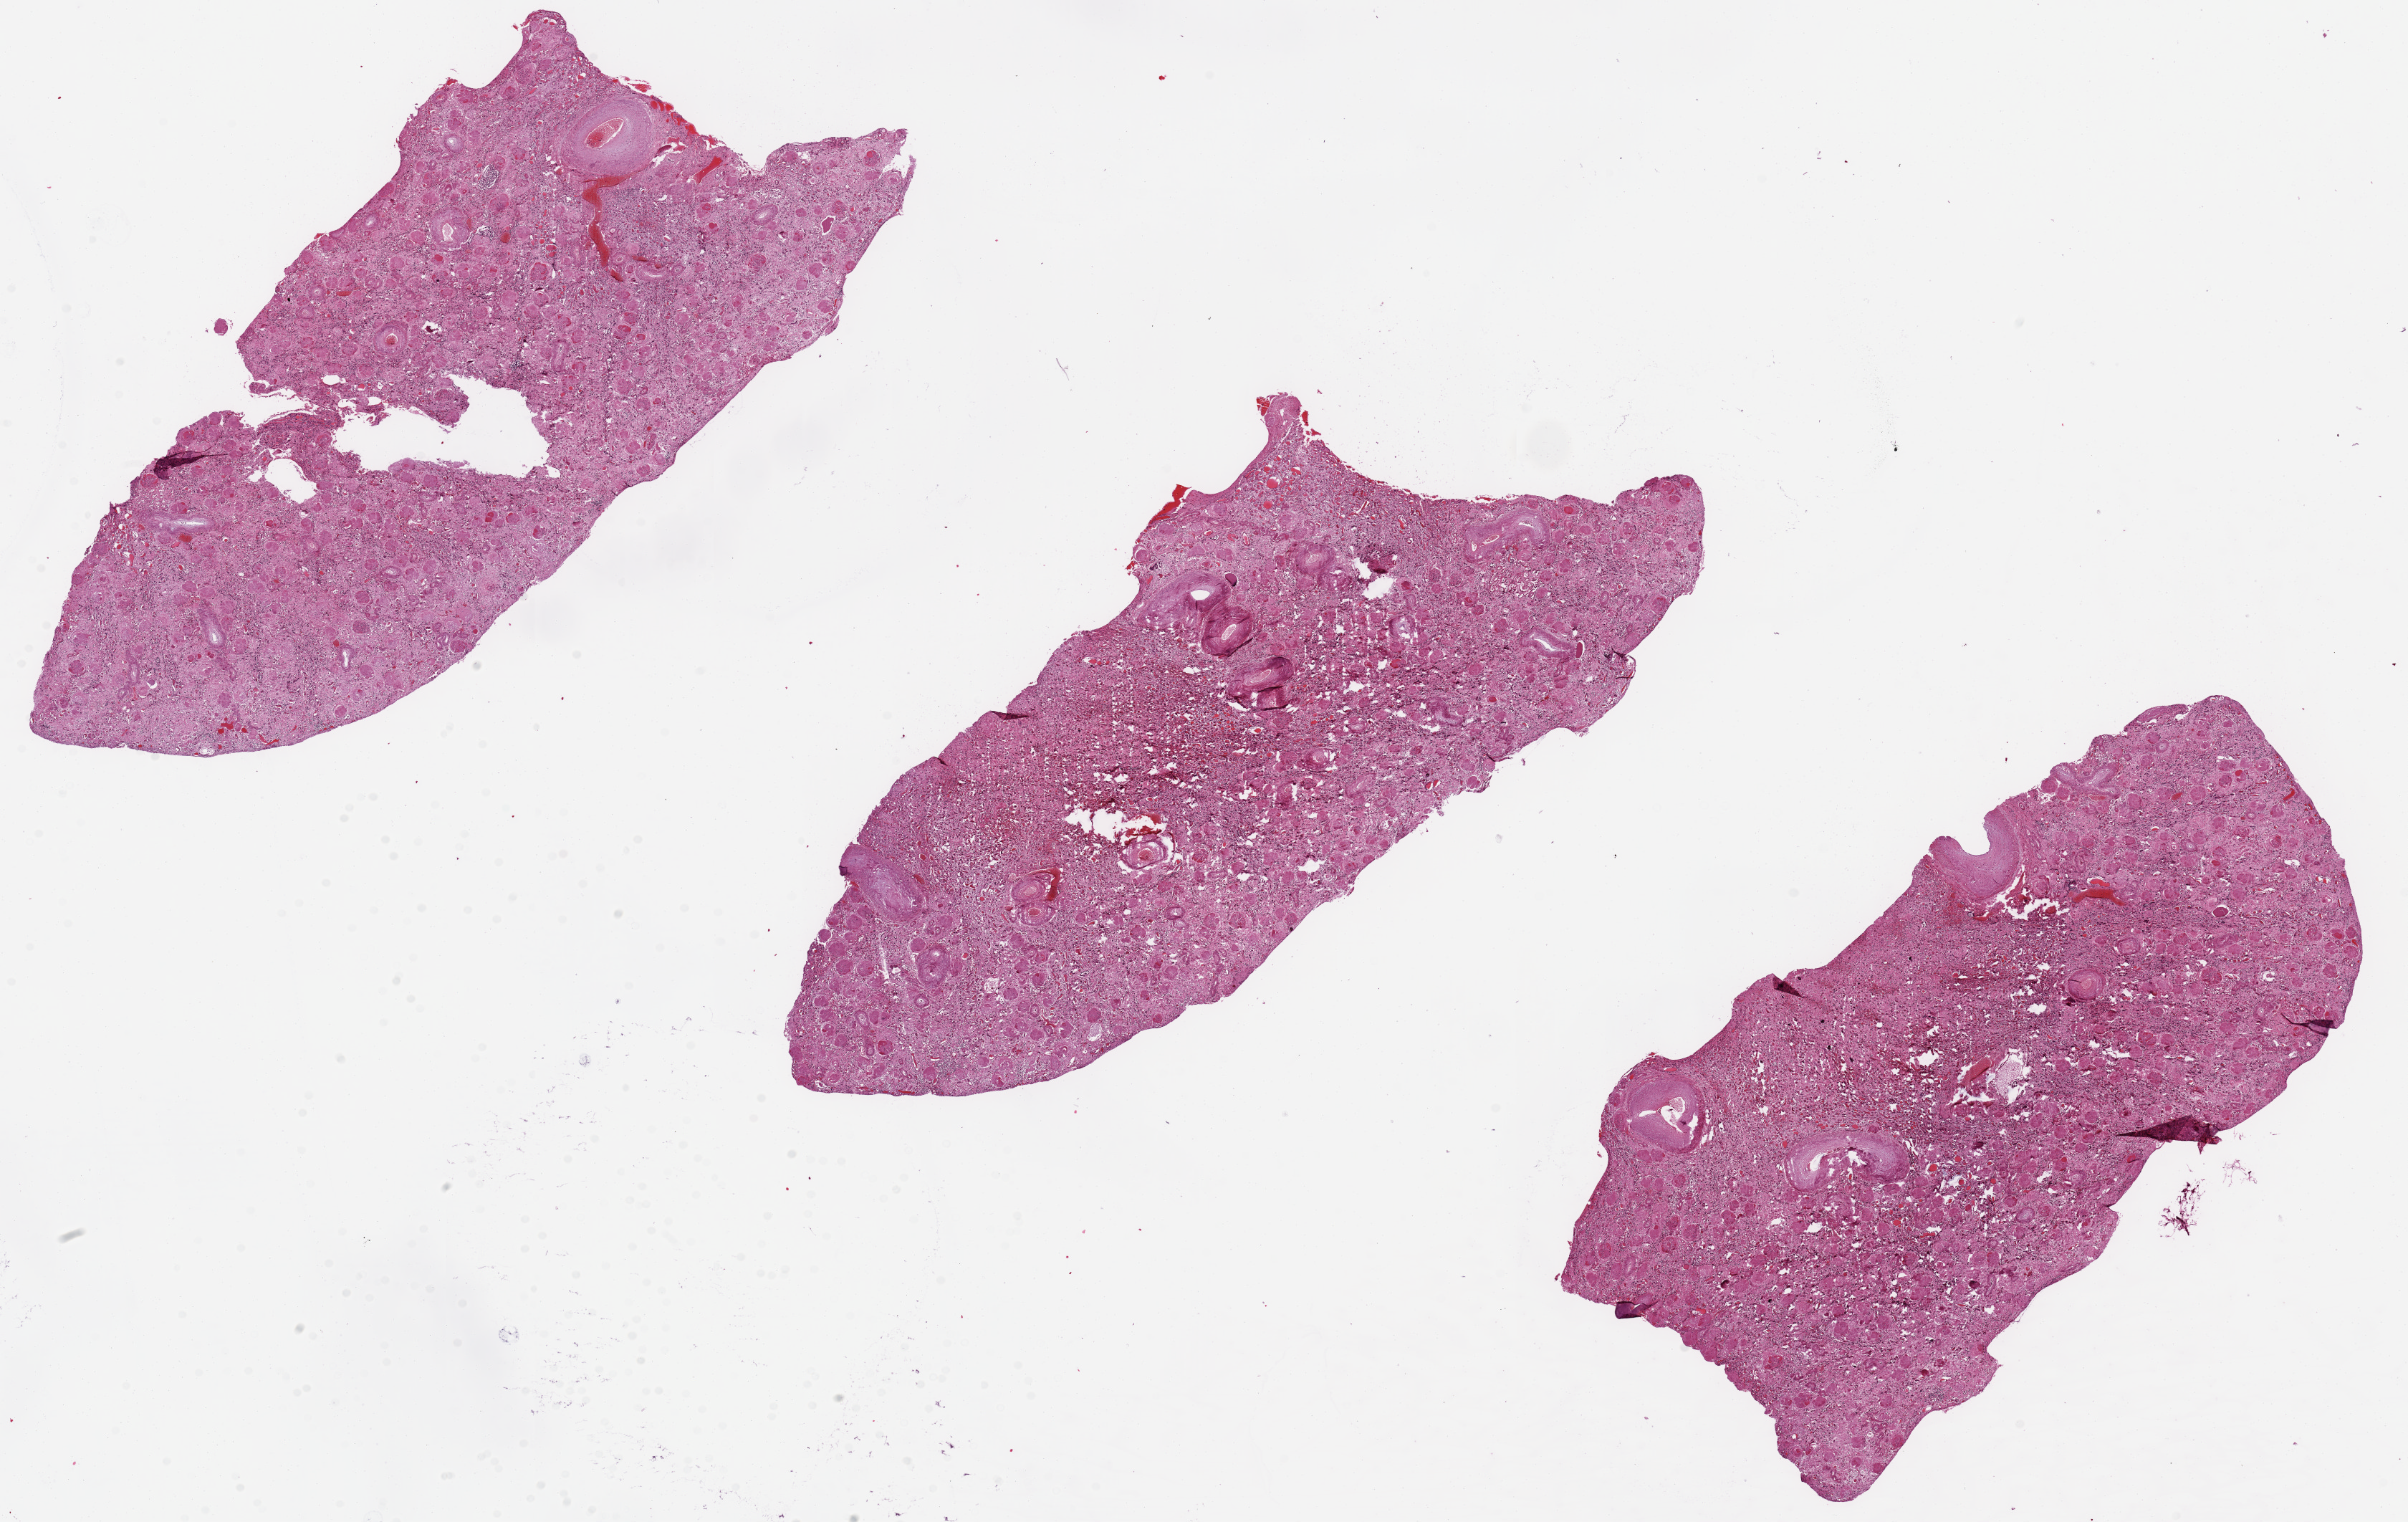
H&E whole-slide image, brightfield — shown as a low-resolution overview of the whole scanned area (about 26.6 x 16.8 mm), PAXgene-fixed paraffin-embedded (PFPE) section, section of renal cortex (target tissue), donor tissue sample. Donor sex: female.
Reviewer comment on this tissue sample: End stage glomerulosclerosis with 100% sclerotic glomeruli; moderate autolysis (???score 2???); nodular sclerosis, probable diabetic. (See Request).